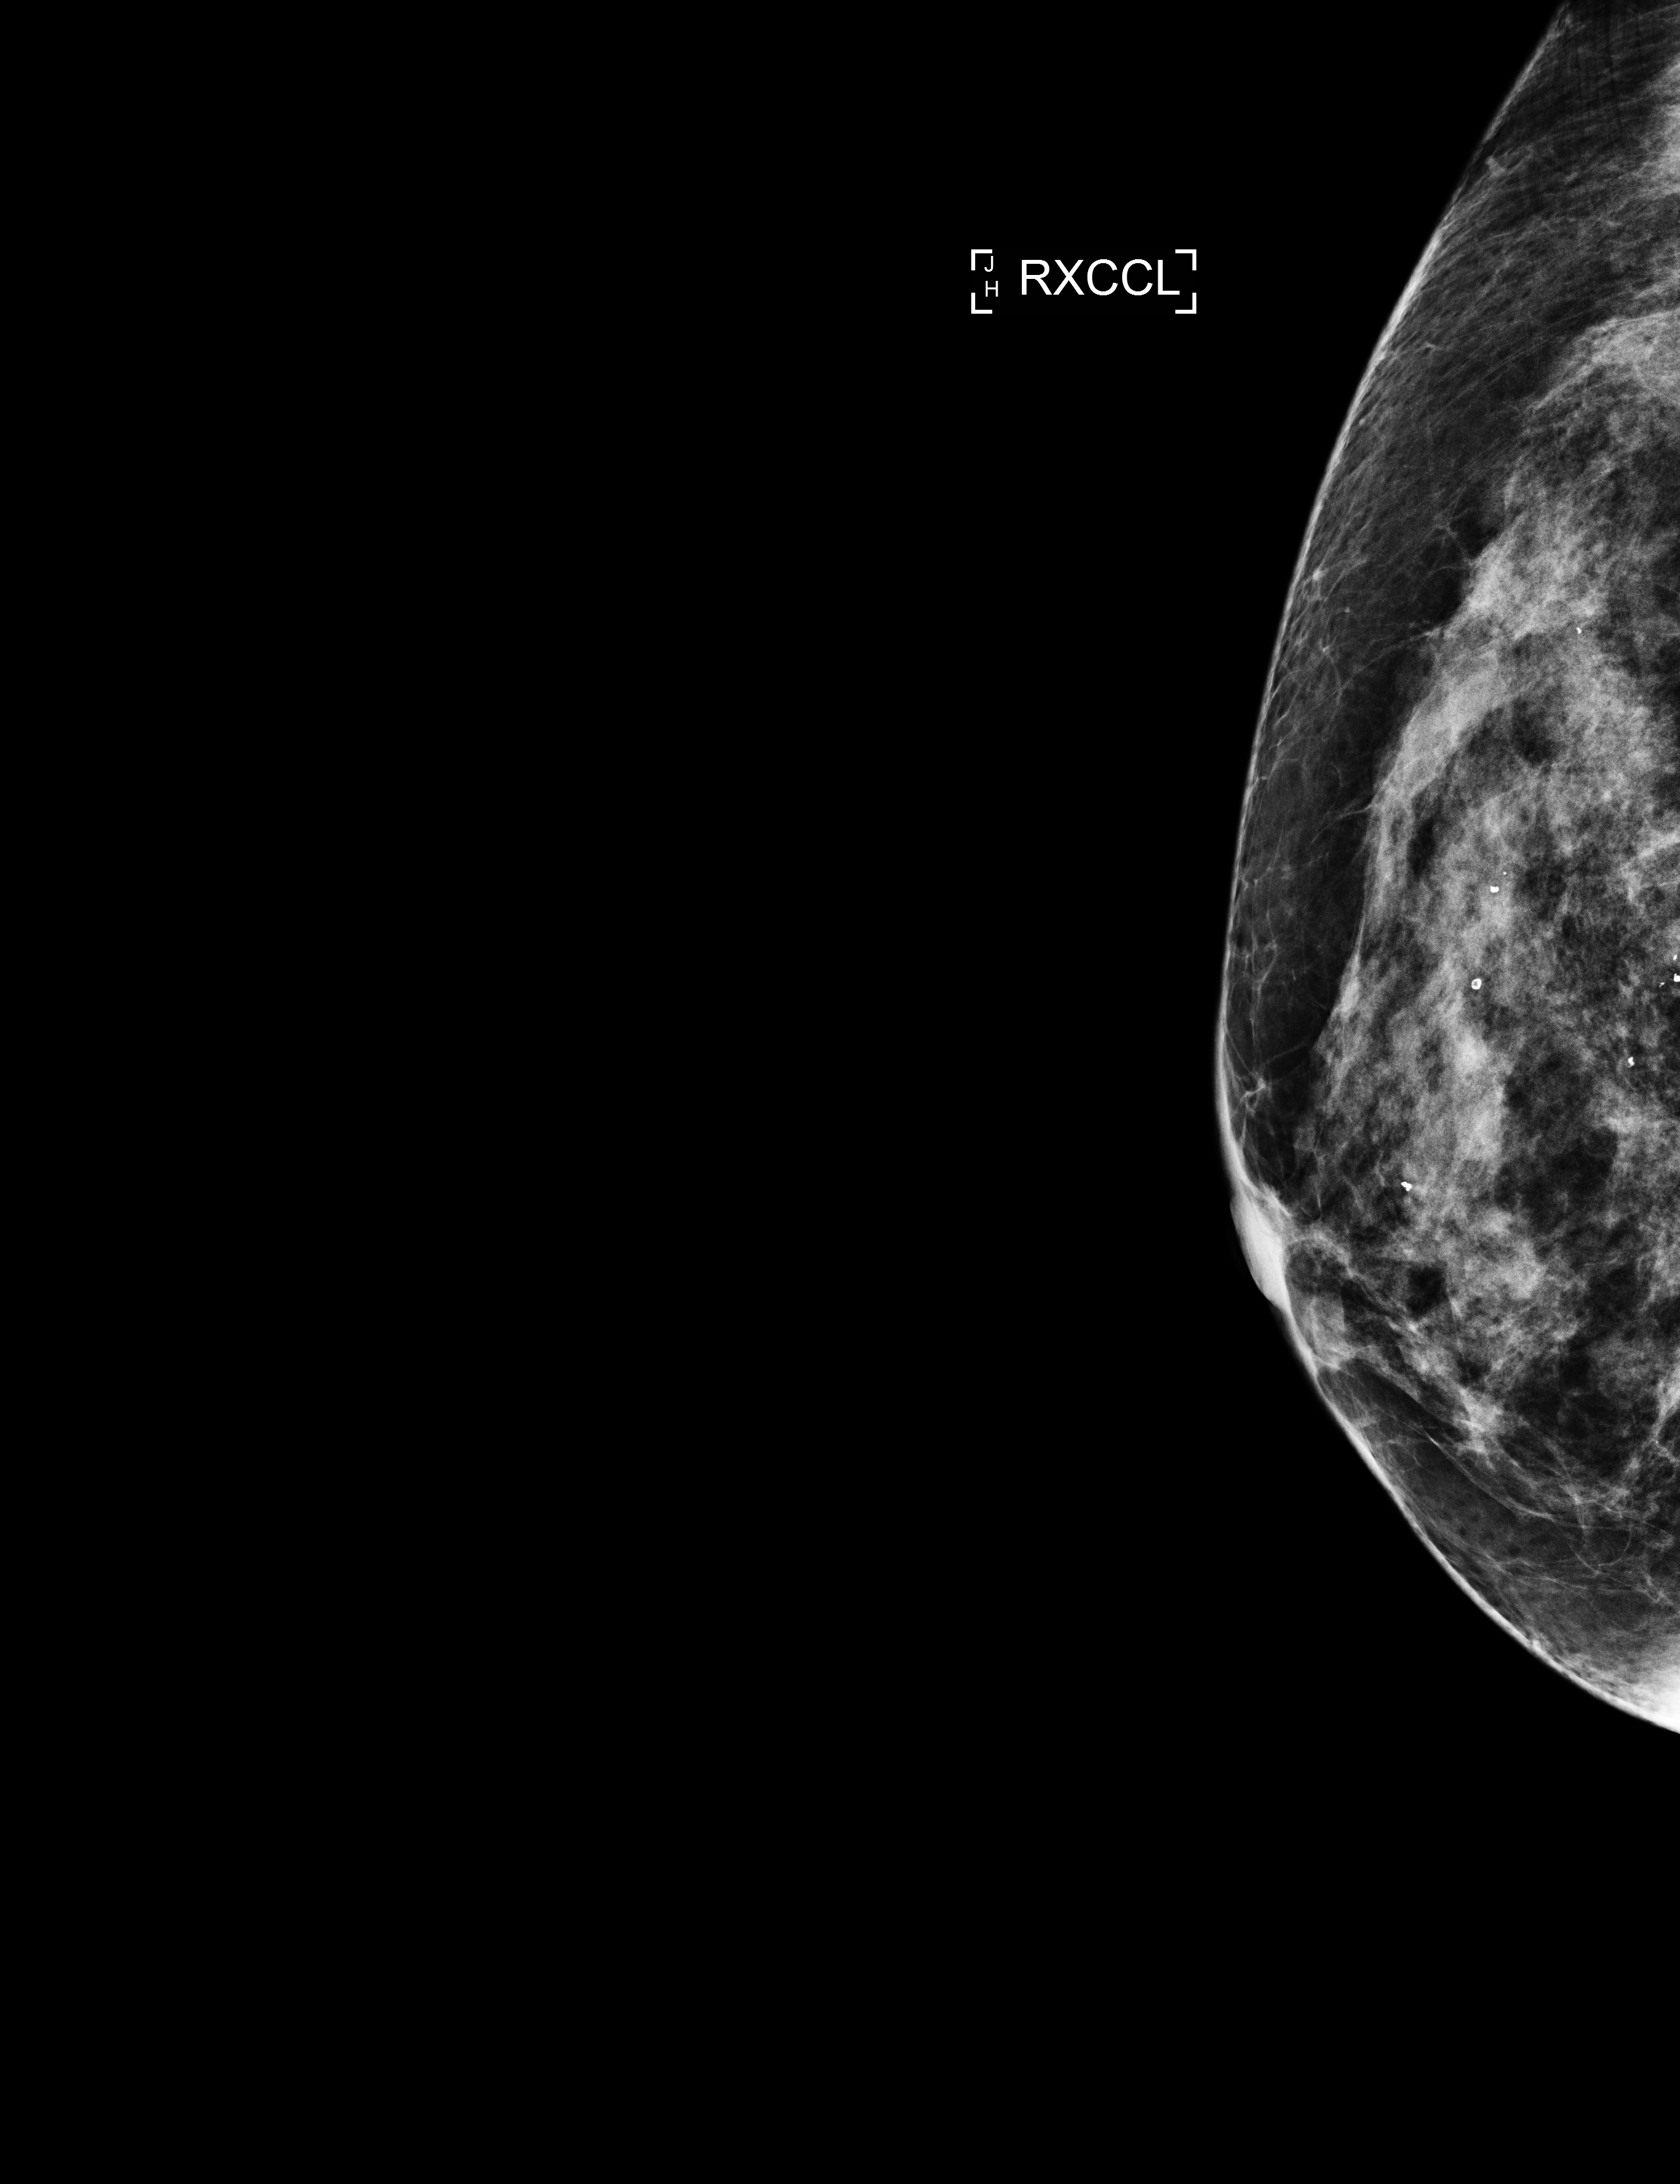
Full-field digital mammogram (FFDM), right breast, laterally exaggerated craniocaudal (XCCL) view, annual screening mammography examination, system: Selenia Dimensions. Patient: female, 74 years.
BI-RADS breast density category at the screening exam (both breasts, scale 1–4): 3. Final BI-RADS category for the screening round (tomosynthesis exam, both breasts): category 2. Recall: no recall after this screen.